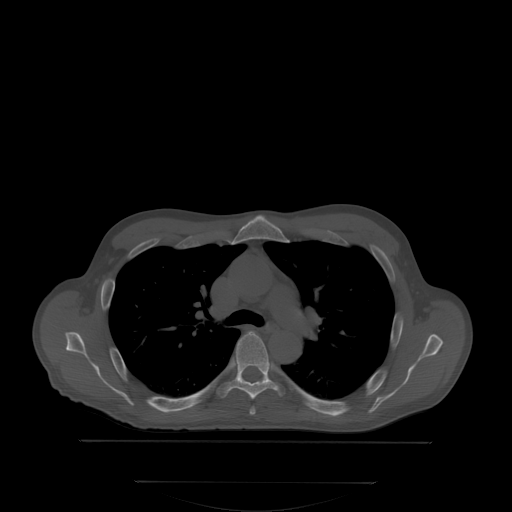
CT including the spine, one axial slice. Slice 248 of 350 in the series (ordered by position). Bone window (W 1800 / L 400 HU). 2.5 mm slice thickness. 512 × 512 image matrix. Patient: male, 58 years. From the clinical record (not read from this slice): primary cancer: prostate; vertebrae with lytic lesions (as recorded): L1.
Annotated regions visible in this slice (semi-automatic segmentation, software-assisted and operator-edited):
- T4 vertebra: bounding box <252,407,255,413> (left, top, right, bottom; pixels)
- T5 vertebra: <217,331,286,399>